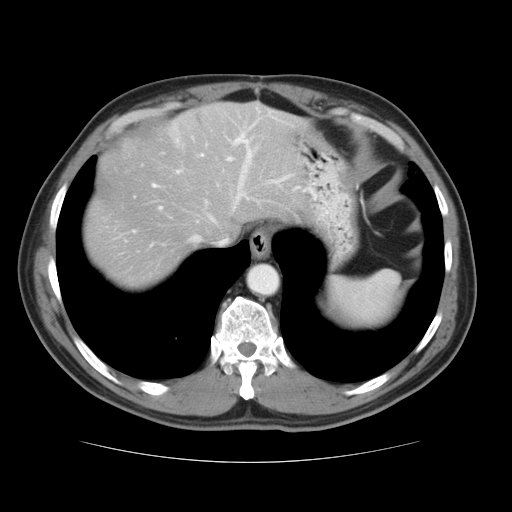
Contrast-enhanced abdominal CT, one axial slice. Slice 30 of 37 in the series (ordered by position). Reconstruction kernel STANDARD. Intravenous contrast given. Soft-tissue window (W 400 / L 40 HU). 5 mm slice thickness. 512 × 512 image matrix. Male patient, age 66 years. Case-level facts recorded for this patient, not image findings: diagnosis: colorectal cancer liver metastases, imaged before liver resection; multiple liver metastases: yes; largest metastasis: 1.6 cm; disease in both lobes: yes.
Outlined on this slice (manually delineated by an expert):
- hepatic veins: bounding box (x1, y1, x2, y2) in pixels: (191, 152, 287, 244)
- liver: (84, 103, 312, 289)
- planned liver remnant (the part of the liver to remain after resection): (84, 108, 312, 289)
- portal vein (with intrahepatic branches): (133, 130, 250, 232)